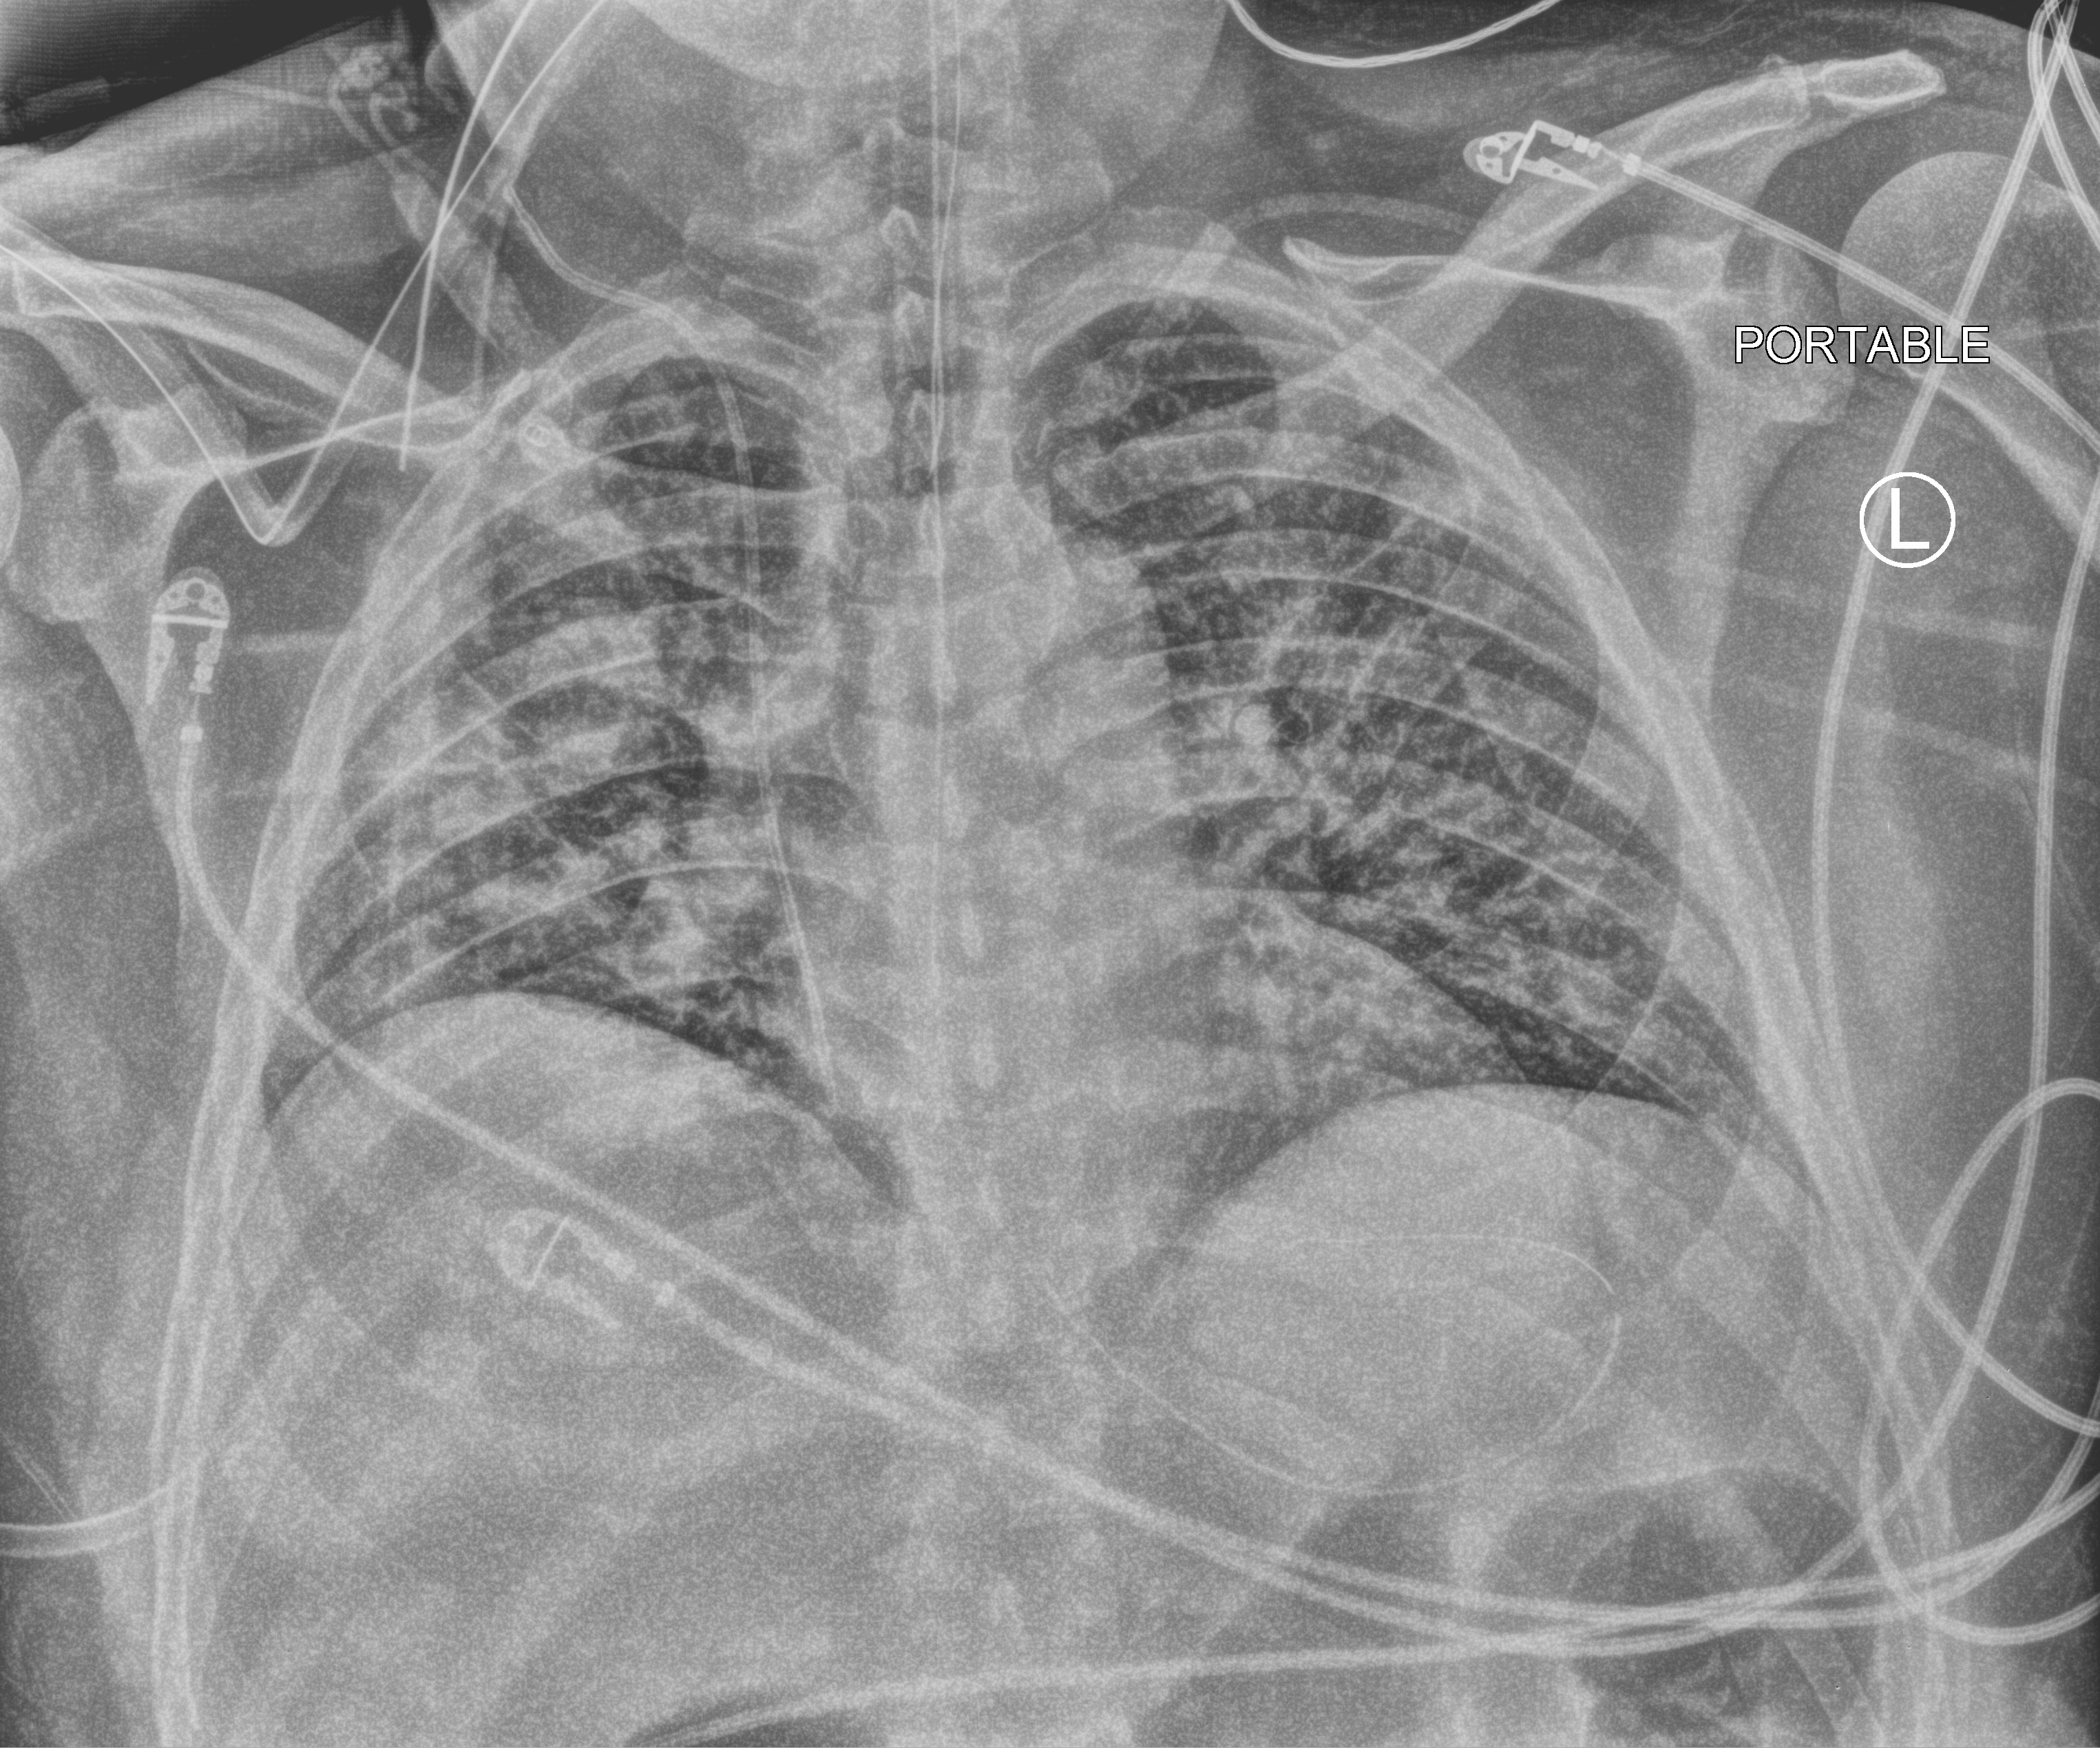
Portable chest radiograph; anteroposterior (AP) projection. Patient hospitalised with COVID-19; male, aged 18–59 years.
Admission-level facts for this patient (not findings on this image; timing relative to this image not recorded): mechanically ventilated during this hospital stay: yes.